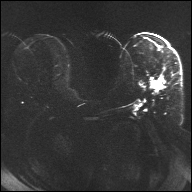
Breast MRI, one axial slice; slice 13 of 32 in the series (ordered by position); diffusion-weighted series; image 2 of 4 stored at this slice position (different b-values; order by instance number); 1.5 T; 4 mm slice thickness; 192 × 192 image matrix, field of view 360 × 360 mm. Female patient.
Outlined on this slice (outlined manually by an expert reader):
- tumour on diffusion-weighted imaging: bounding box (x1, y1, x2, y2) in pixels: (151, 78, 164, 89)